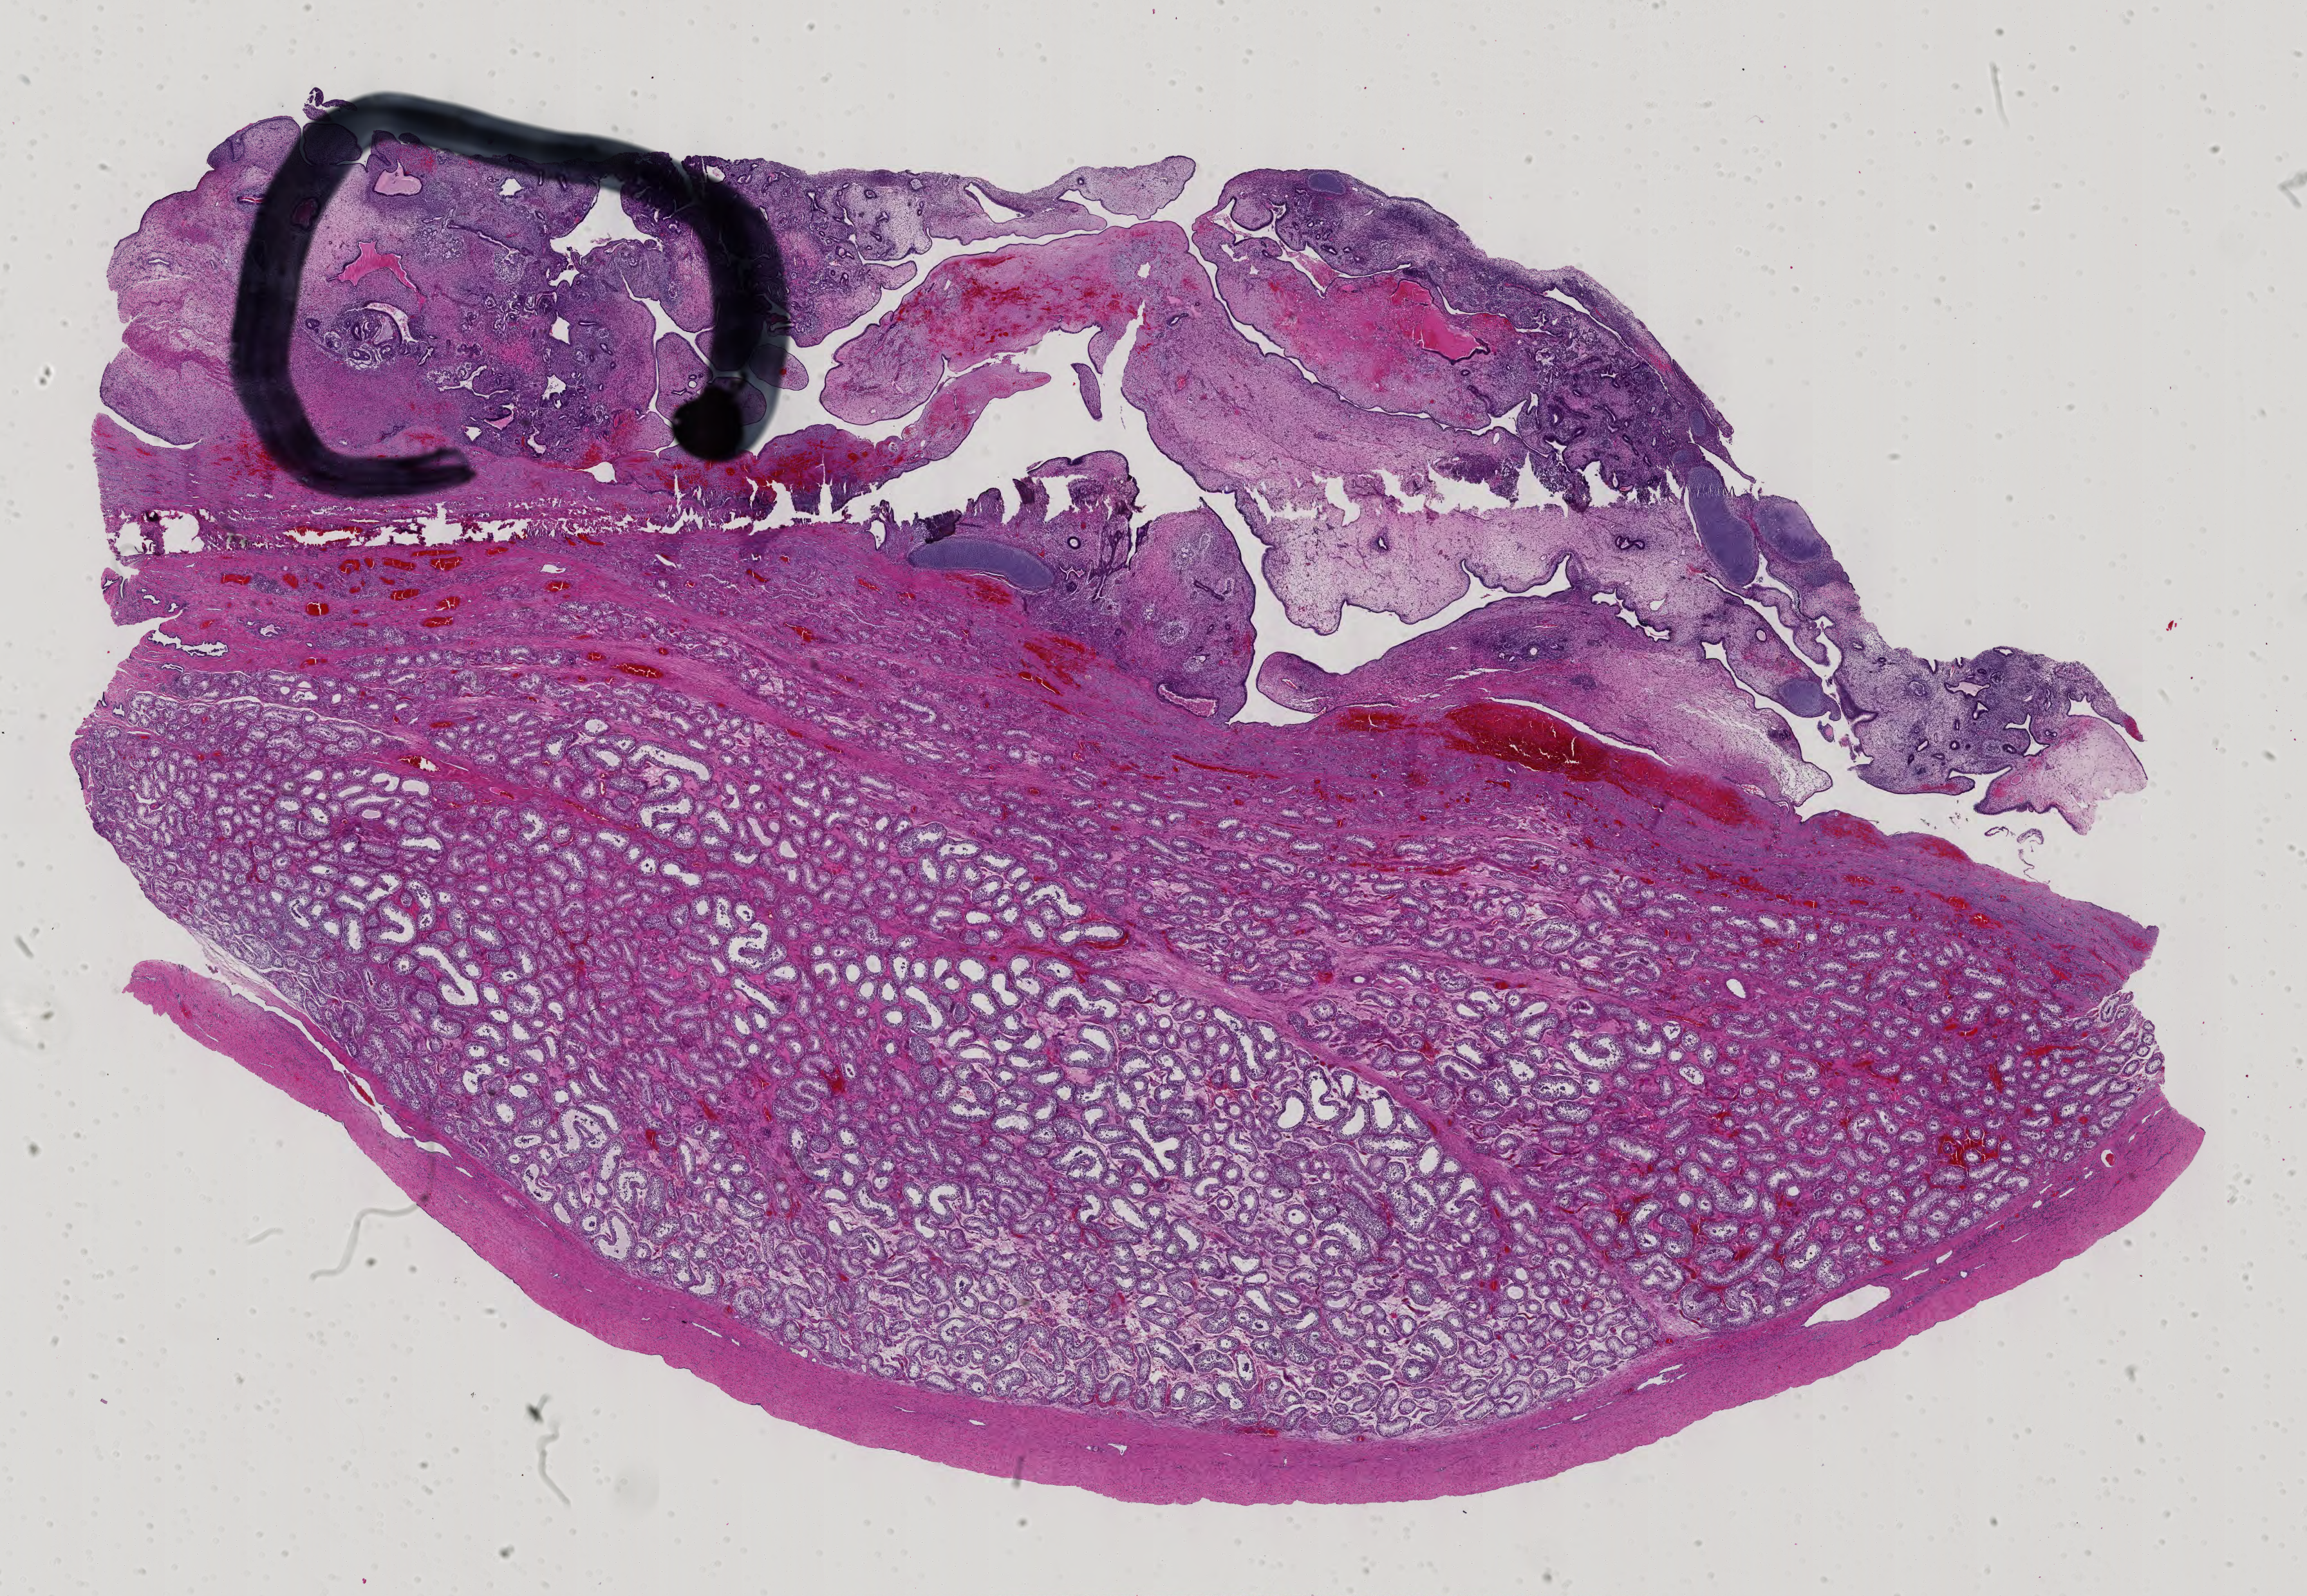
H&E-stained whole-slide image, whole scanned area (about 26.1 x 18.1 mm, slide scanned at 40x) shown as a low-resolution overview; formalin-fixed paraffin-embedded (FFPE) diagnostic section; sample: primary tumour, testis. Male patient; age at initial diagnosis 23 years.
Histologic diagnosis: Teratoma, malignant, NOS.